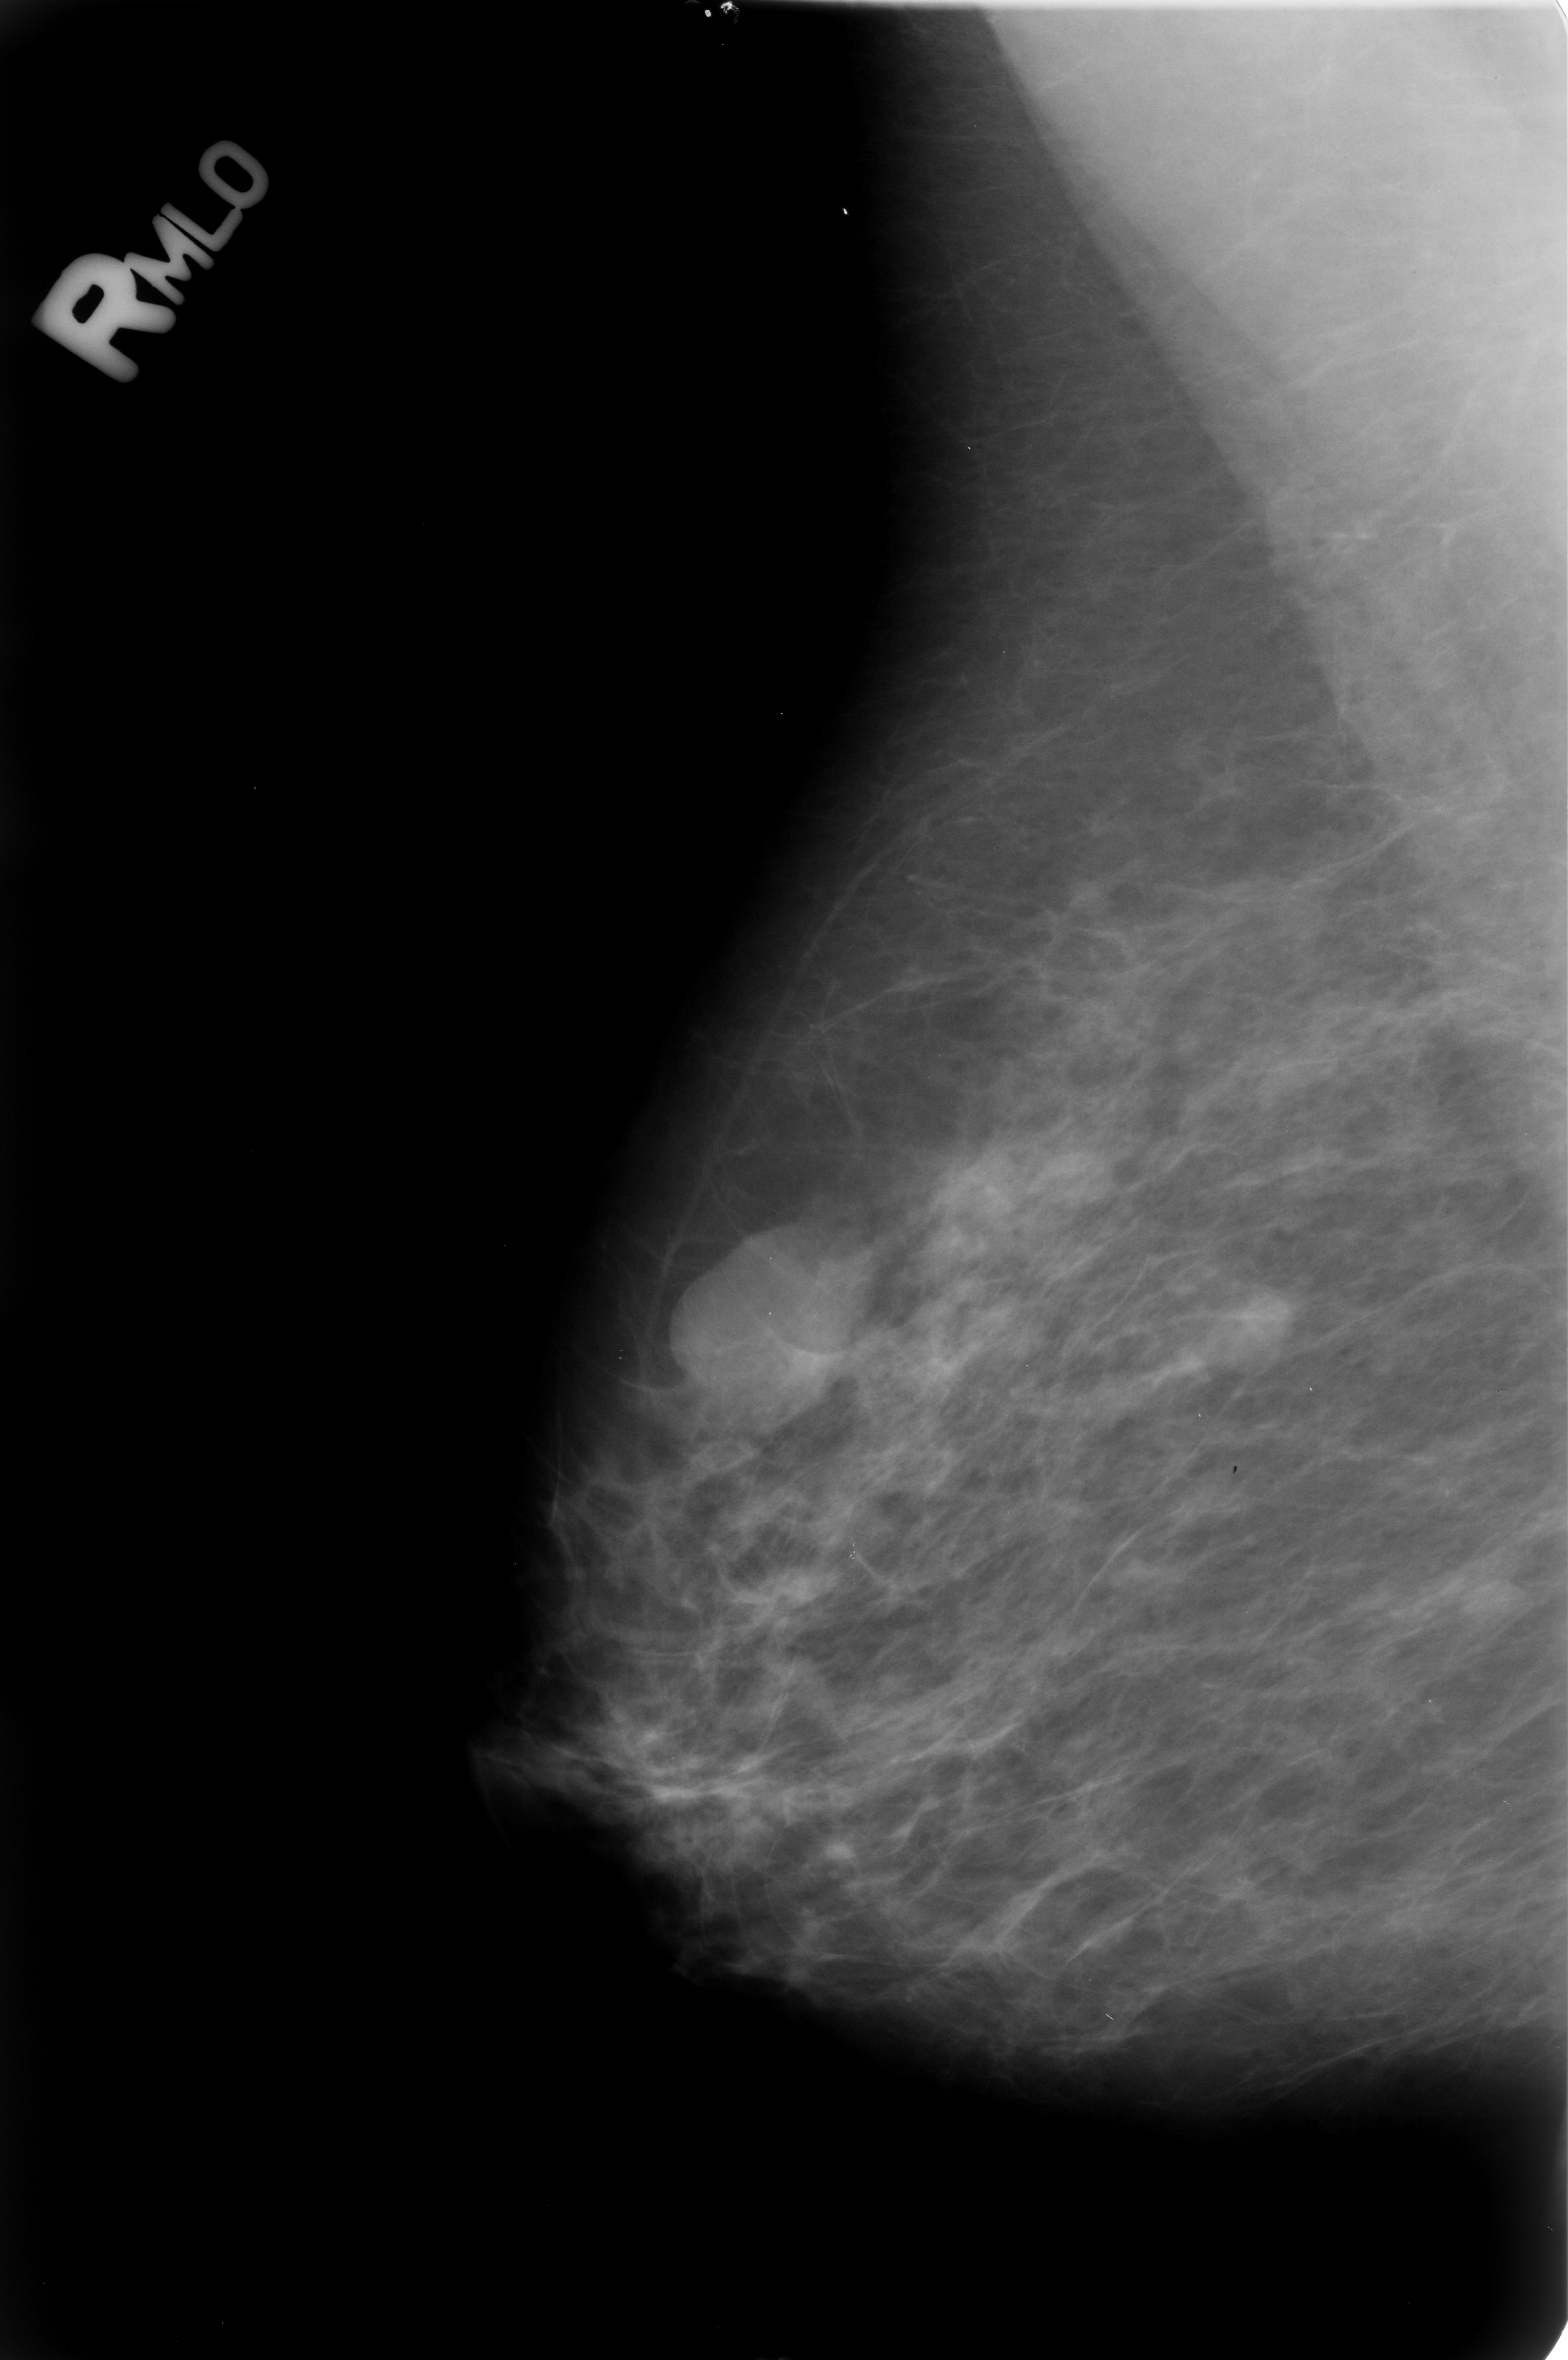
Scanned film-screen mammogram; right breast; MLO view; 1568 × 2360 image matrix.
Expert-marked regions of interest on this image (one box per marked abnormality):
- mass, shape lobulated, margins circumscribed / obscured; BI-RADS assessment category 4; pathology (as recorded): benign: bounding box [x1, y1, x2, y2] px = [1193, 1279, 1309, 1377]